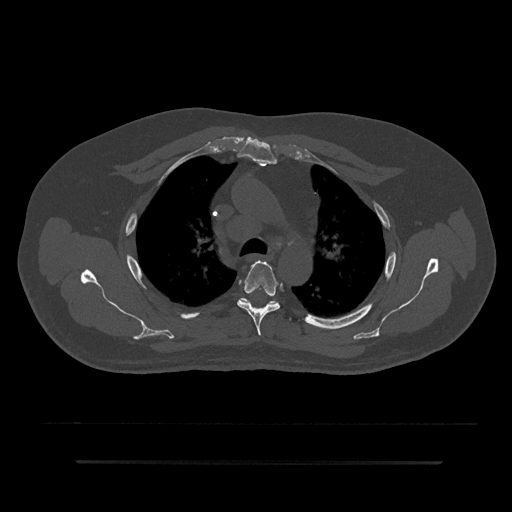
CT including the spine, one axial slice; slice 611 of 797 in the series (ordered by position); 120 kVp; bone window (W 1800 / L 400 HU); 512 × 512 image matrix, field of view 464 × 464 mm. Patient: male, 59 years. Case-level facts recorded for this patient, not image findings: primary cancer: bile ducts.
Outlined on this slice (semi-automatically segmented with operator editing):
- T4 vertebra: bounding box [x1, y1, x2, y2] px = [237, 261, 280, 336]
- T5 vertebra: [237, 298, 279, 305]